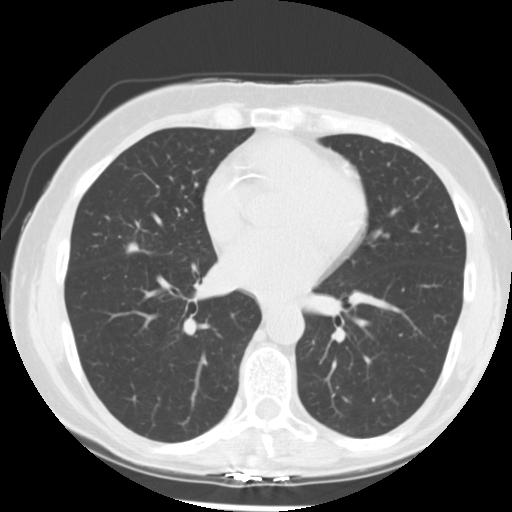
Low-dose screening chest CT, one axial slice. Slice 127 of 255 in the series (ordered by position). Reconstruction kernel STANDARD. Lung window (W 1500 / L -600 HU). 2.5 mm slice thickness. 512 × 512 image matrix.
Structures marked on this image (manually delineated by an expert):
- lesion 1 (tumor, middle lobe of right lung): bounding box (x1, y1, x2, y2) in pixels: (127, 243, 138, 252)